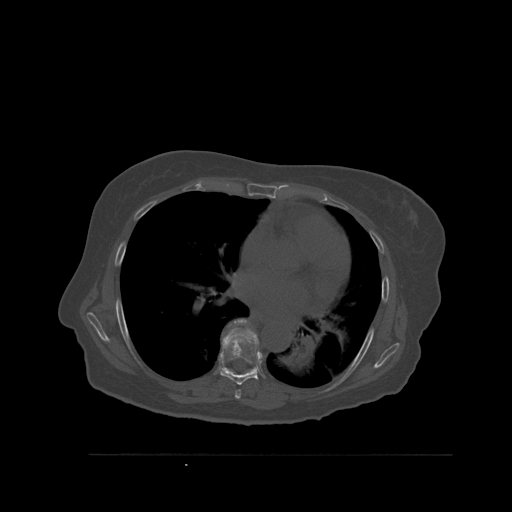
CT including the spine, one axial slice. Position 363 of 527 along the scan axis. Bone window (W 1800 / L 400 HU). 512 × 512 image matrix, field of view 470 × 470 mm. Female patient, age 73 years. Case-level facts recorded for this patient, not image findings: primary cancer: breast; vertebrae with lytic lesions (as recorded): L2.
Annotated regions visible in this slice (semi-automatically segmented with operator editing):
- T6 vertebra: box from (x=235, y=390) to (x=241, y=399) px
- T7 vertebra: (x=220, y=330)–(x=262, y=385)
- T8 vertebra: (x=222, y=319)–(x=256, y=373)